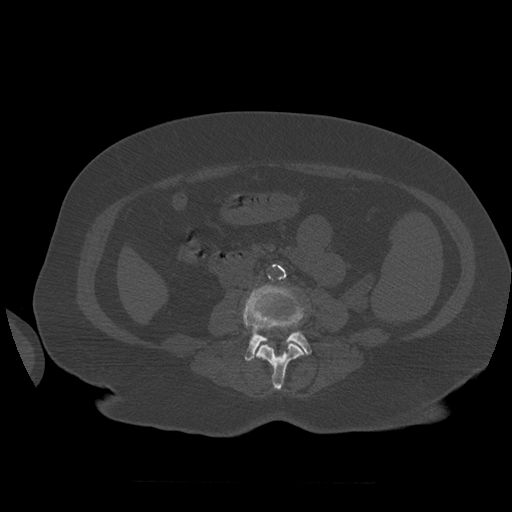
CT including the spine, one axial slice; reconstruction kernel STANDARD; bone window (W 1800 / L 400 HU); 512 × 512 image matrix, field of view 404 × 404 mm. Patient age 81 years. Case-level facts recorded for this patient, not image findings: primary cancer: renal; vertebrae with lytic lesions (as recorded): L1.
Annotated regions visible in this slice (semi-automatically segmented with operator editing):
- L3 vertebra: bounding box (x1, y1, x2, y2) in pixels: (255, 342, 305, 390)
- L4 vertebra: (244, 285, 312, 361)